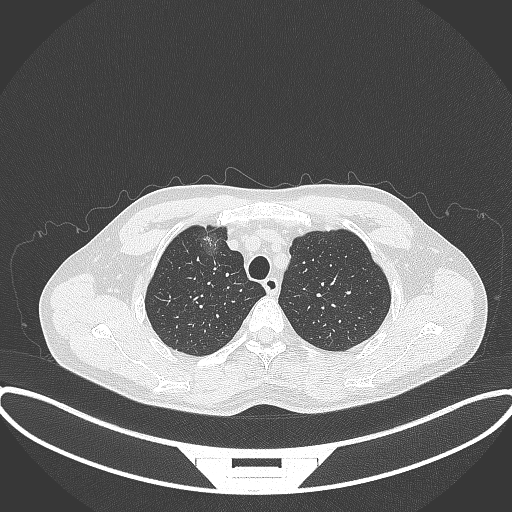
Chest CT, one axial slice. Slice 299 of 395 in the series (ordered by position). Reconstruction kernel B70f. Lung window (W 1500 / L -600 HU). 1 mm slice thickness. 512 × 512 image matrix, field of view 424 × 424 mm. Patient: male, 60 years. From the clinical record (not read from this slice): clinical TNM (as recorded): T1c N0 M0.
Structures marked on this image (bounding box drawn by a radiologist):
- lung tumour (recorded histology: adenocarcinoma): bounding box <195,222,226,264> (left, top, right, bottom; pixels)